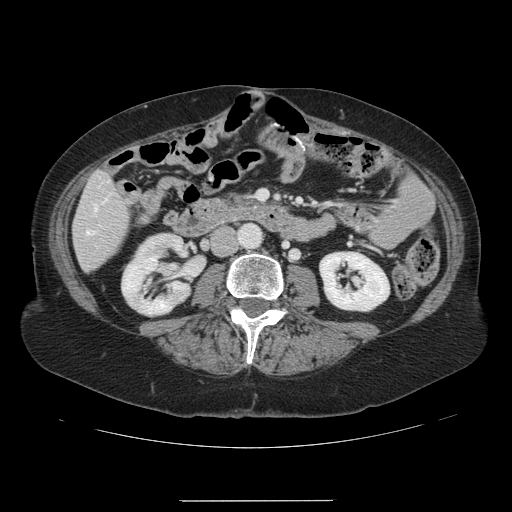
Contrast-enhanced abdominal CT, one axial slice; slice 29 of 141 in the series (ordered by position); 120 kVp; intravenous contrast given; soft-tissue window (W 400 / L 40 HU); 512 × 512 image matrix, field of view 393 × 393 mm. Female patient, age 74 years. From the clinical record (not read from this slice): diagnosis: colorectal cancer liver metastases, imaged before liver resection; multiple liver metastases: yes; largest metastasis: 7 cm; disease in both lobes: yes.
Structures marked on this image (expert manual segmentation):
- hepatic veins: box from (x=86, y=207) to (x=97, y=234) px
- liver: (x=74, y=173)–(x=130, y=271)
- planned liver remnant (the part of the liver to remain after resection): (x=74, y=173)–(x=109, y=271)